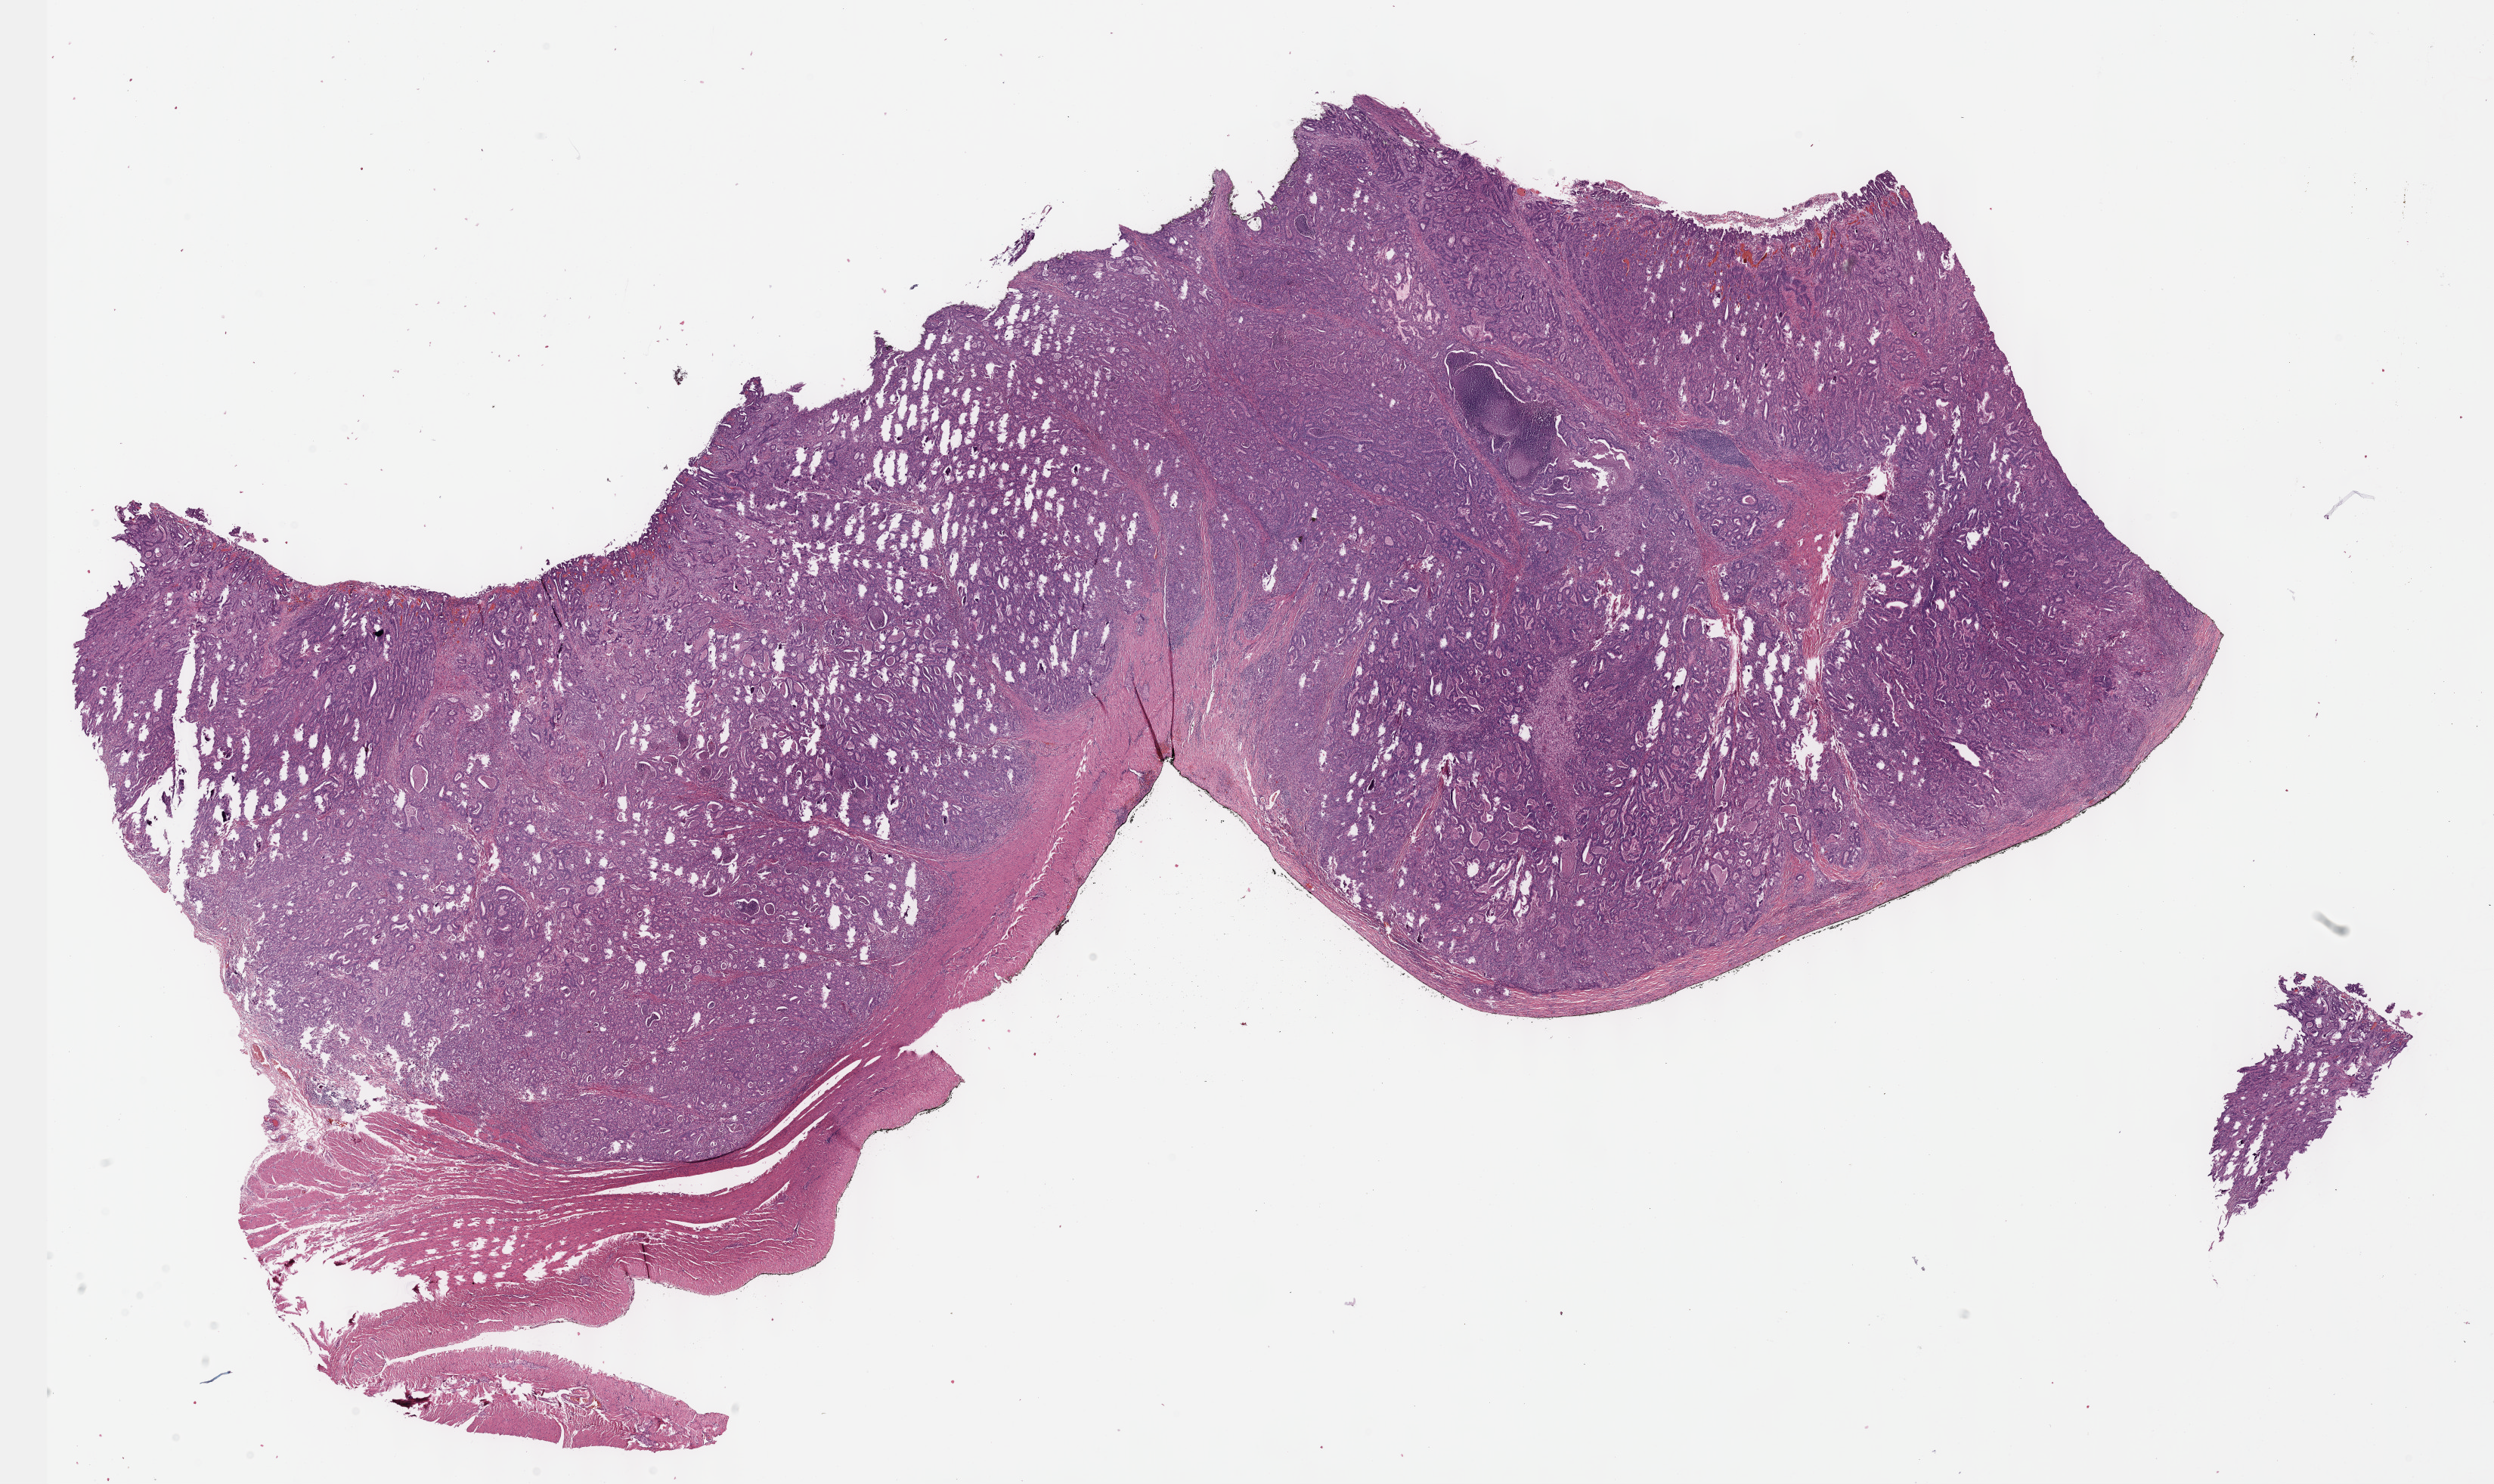
H&E-stained whole-slide image, whole scanned area (about 26.7 x 15.9 mm) shown as a low-resolution overview. FFPE section. Stomach, primary tumour sample. Male, age 69 years at initial diagnosis. Histologic grade: G2 (moderately differentiated).
* lymph nodes positive (case pathology): 0 of 27 examined
* TNM: T3 N0 M0
* pathologic diagnosis: Tubular adenocarcinoma
* AJCC pathologic stage: II (6th edition)